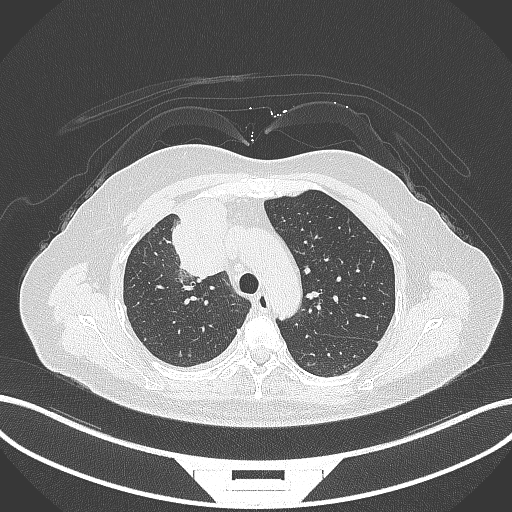
Chest CT, one axial slice; slice 214 of 305 in the series (ordered by position); 120 kVp; lung window (W 1500 / L -600 HU); 512 × 512 image matrix. Patient: female, 52 years. From the clinical record (not read from this slice): clinical TNM (as recorded): T3 N1 M1.
Annotated regions visible in this slice (bounding box drawn by a radiologist):
- lung tumour (recorded histology: adenocarcinoma): bounding box [x1, y1, x2, y2] px = [165, 195, 230, 279]